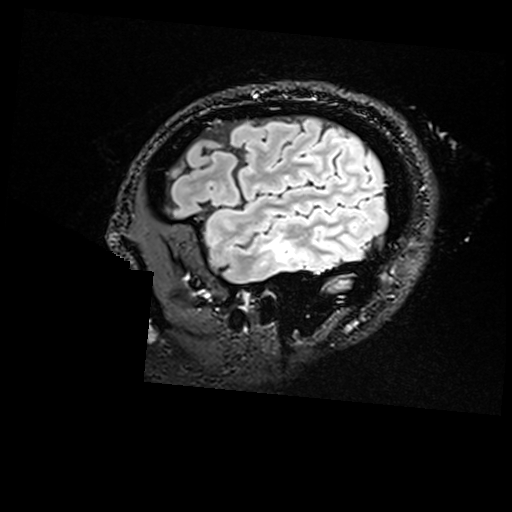
Brain MRI from a brain-tumour surgery series, one sagittal slice; T2 FLAIR; 512 × 512 image matrix, field of view 250 × 250 mm. From the clinical record (not read from this slice): histopathology: Non-tumor destructive chronic inflammatory lesion with abnormal vasculature; tumour location: Right Inferior Temporal.
Structures marked on this image (outlined manually by an expert reader):
- residual tumour: bounding box <280,242,295,259> (left, top, right, bottom; pixels)